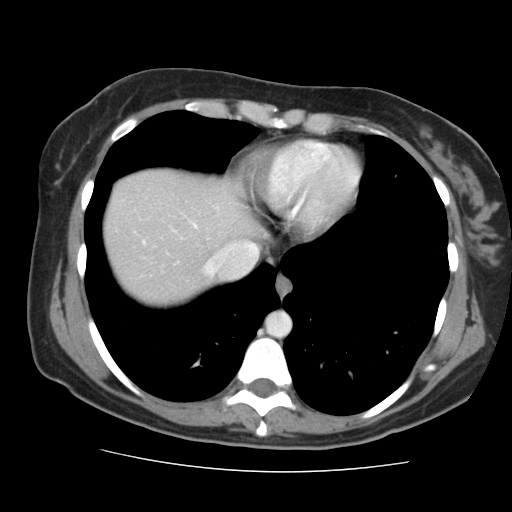
Contrast-enhanced abdominal CT, one axial slice. Slice 134 of 144 in the series (ordered by position). Soft-tissue window (W 400 / L 40 HU). 512 × 512 image matrix, field of view 333 × 333 mm. Female patient, age 46 years. From the clinical record (not read from this slice): diagnosis: colorectal cancer liver metastases, imaged before liver resection; multiple liver metastases: no; largest metastasis: 2.8 cm.
Annotated regions visible in this slice (expert manual segmentation):
- hepatic veins: box from (x=204, y=241) to (x=258, y=277) px
- liver: (x=105, y=171)–(x=257, y=305)
- planned liver remnant (the part of the liver to remain after resection): (x=105, y=171)–(x=257, y=305)